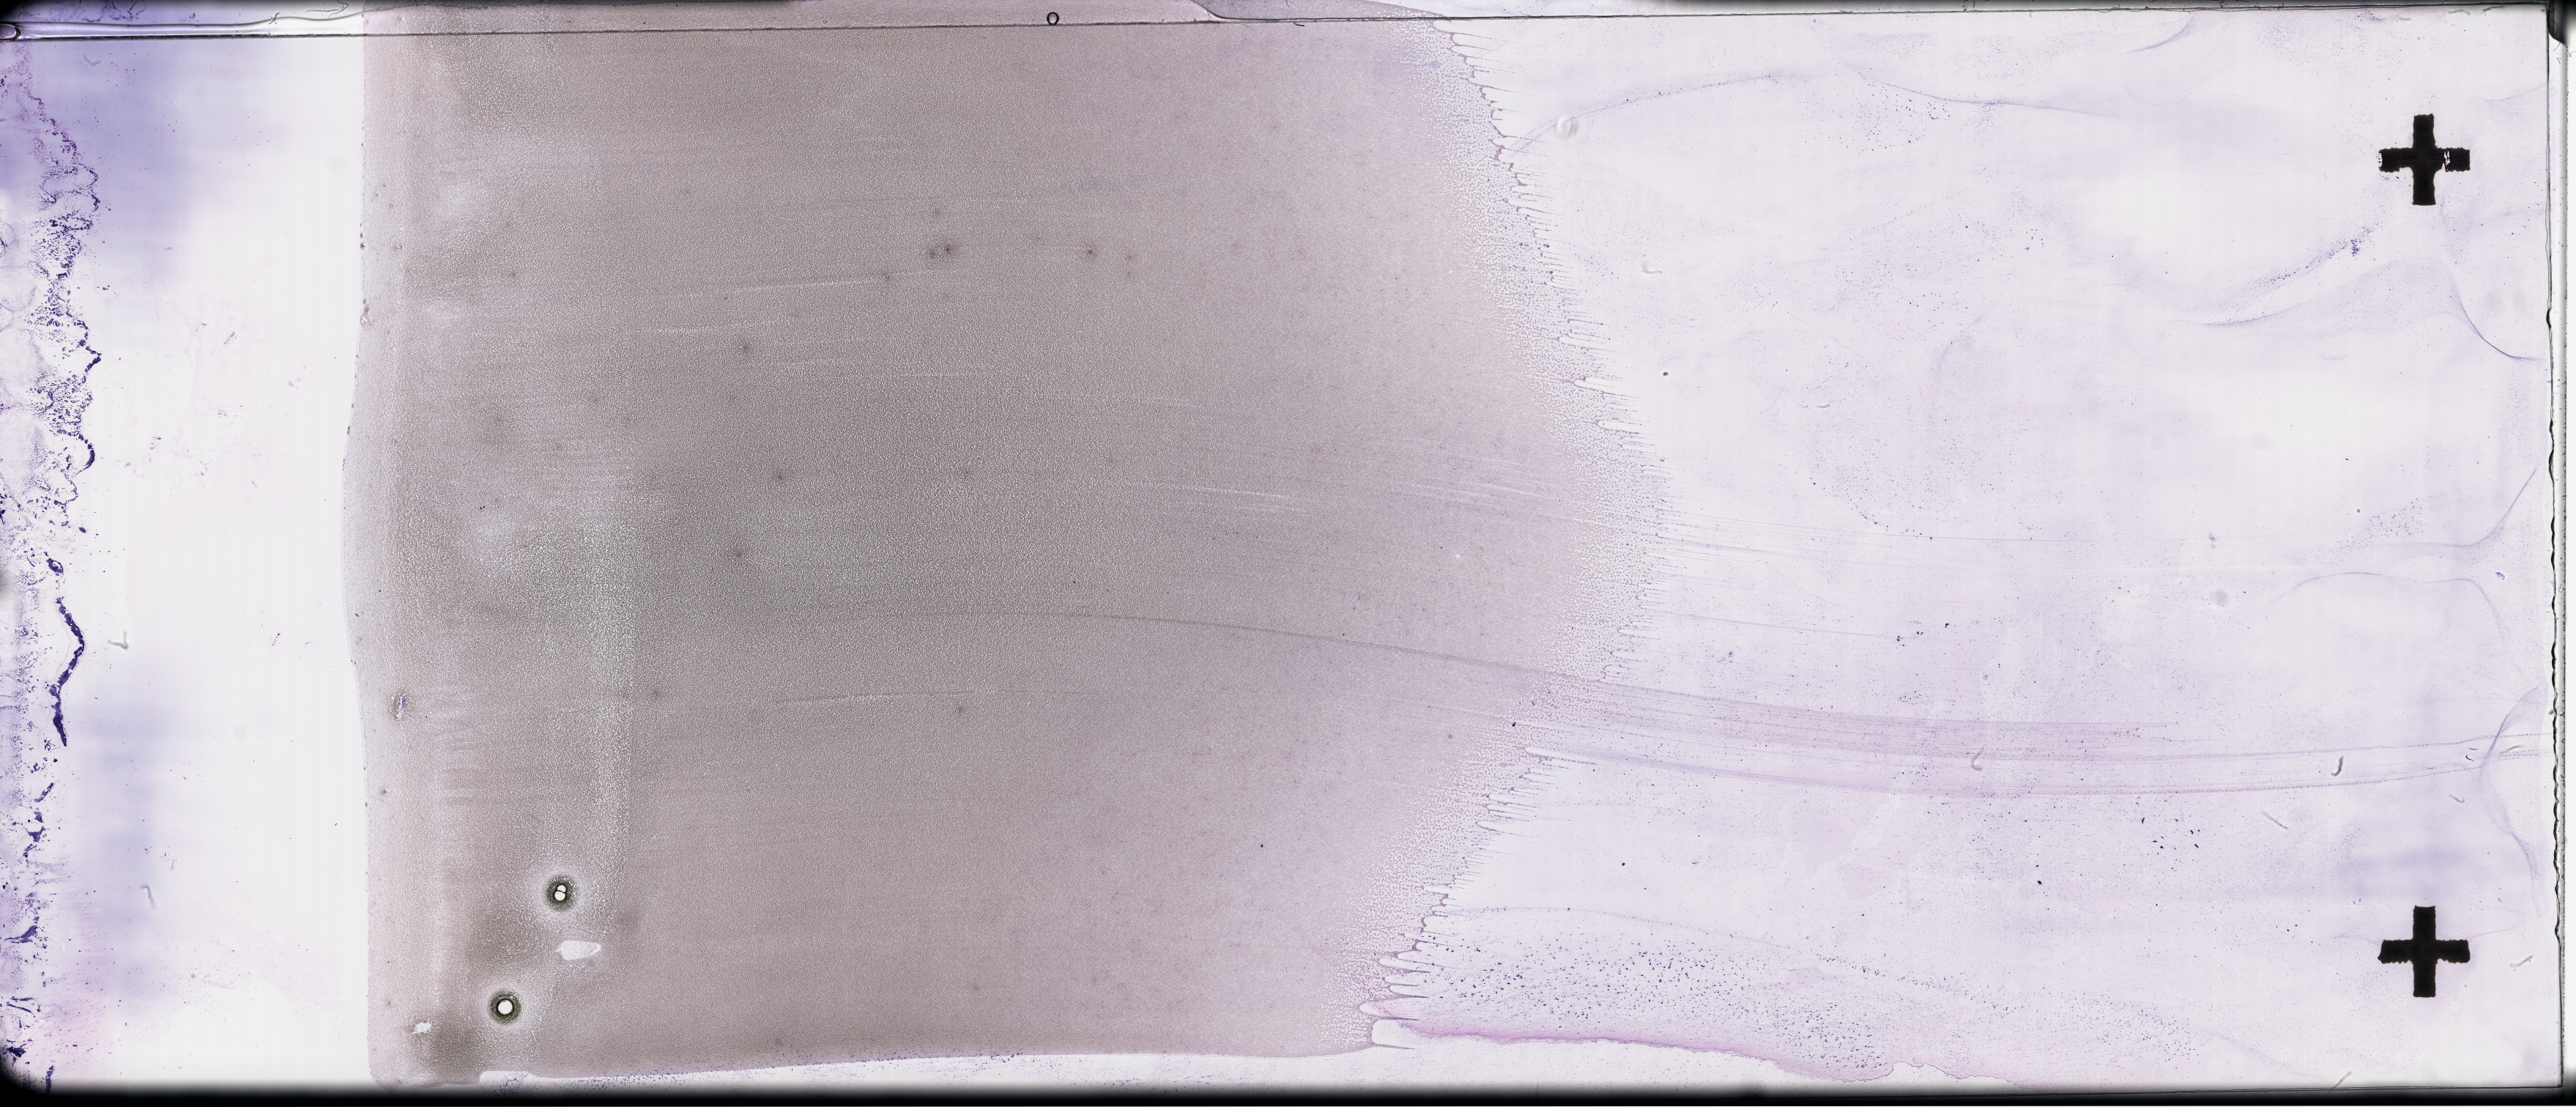
Wright–Giemsa-stained whole blood smear, whole-slide image — a low-resolution overview of the entire scanned area, about 56.8 x 24.4 mm, smear from an EDTA sample, collected post-treatment, no progression. Patient sex: female.
Patient diagnosis: Acute Myeloid Leukemia Not Otherwise Specified.